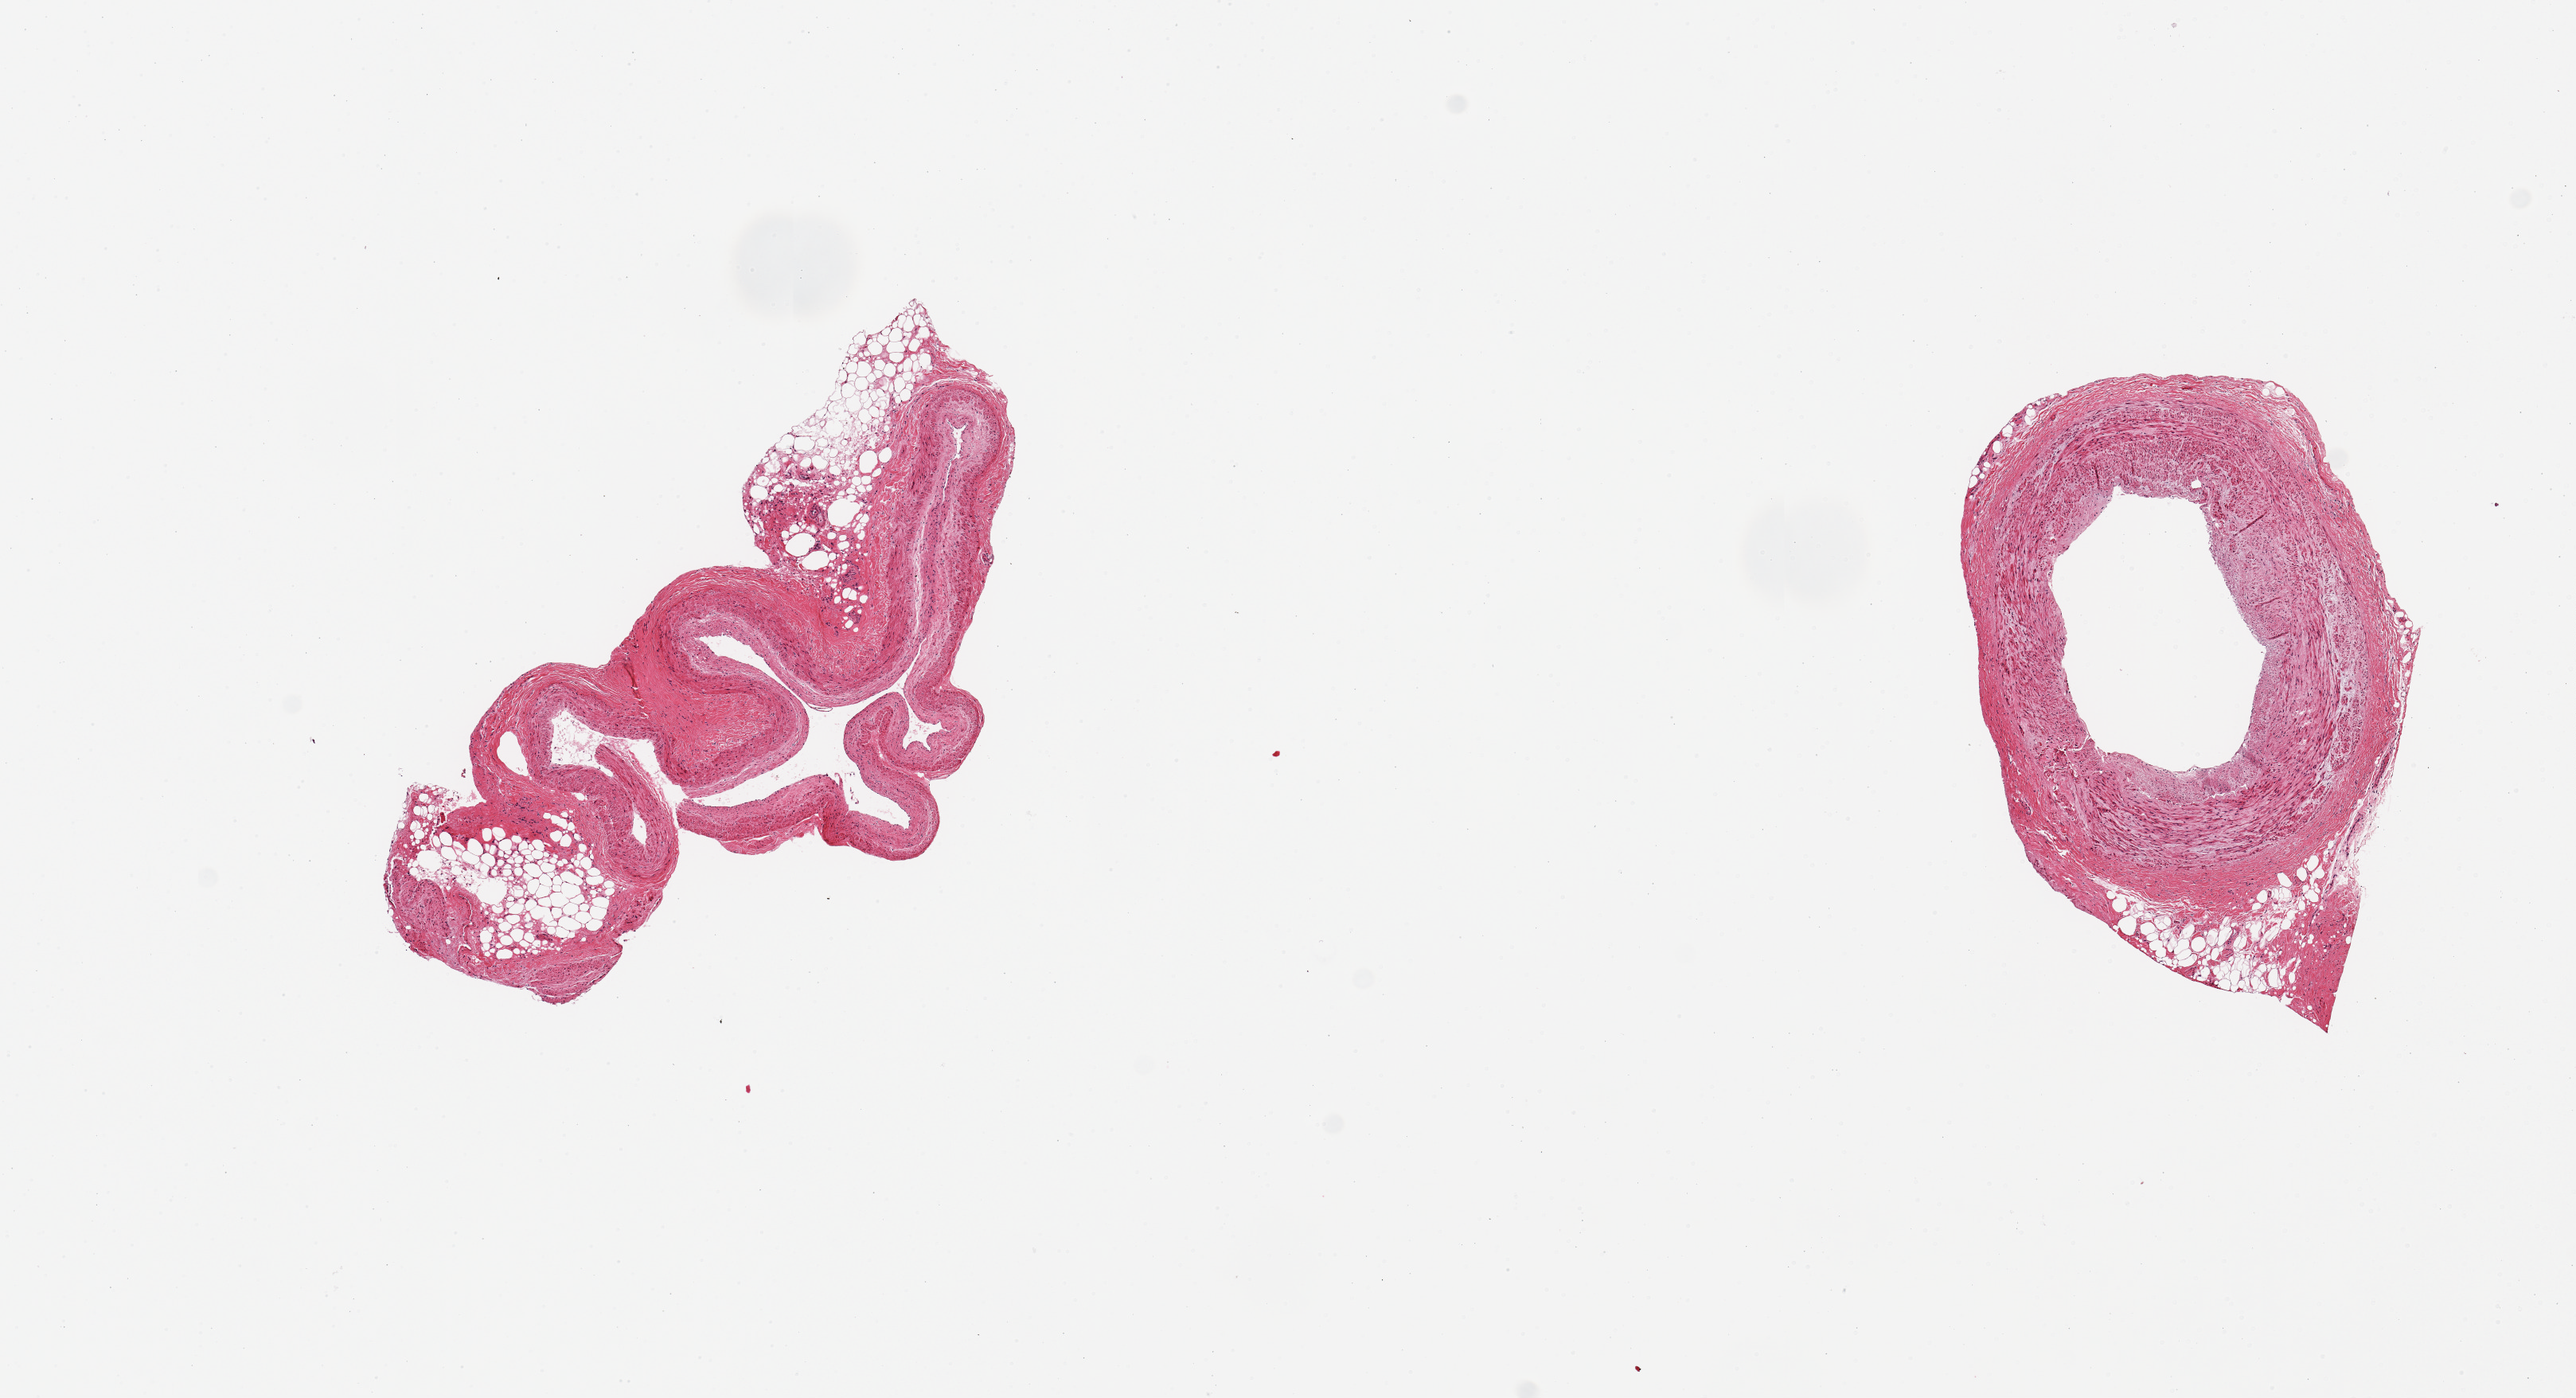
Whole-slide image, H&E stain, shown as a low-resolution overview of the whole scanned area (about 12.8 x 6.9 mm, from a 20x scan). PAXgene-fixed, paraffin-embedded tissue. Section of coronary artery (target tissue). Donor tissue sample. Donor: female.
• reviewer comment on this tissue sample: 2 pieces, no significant atherosis, nubbins of fat up to ~0.8mm